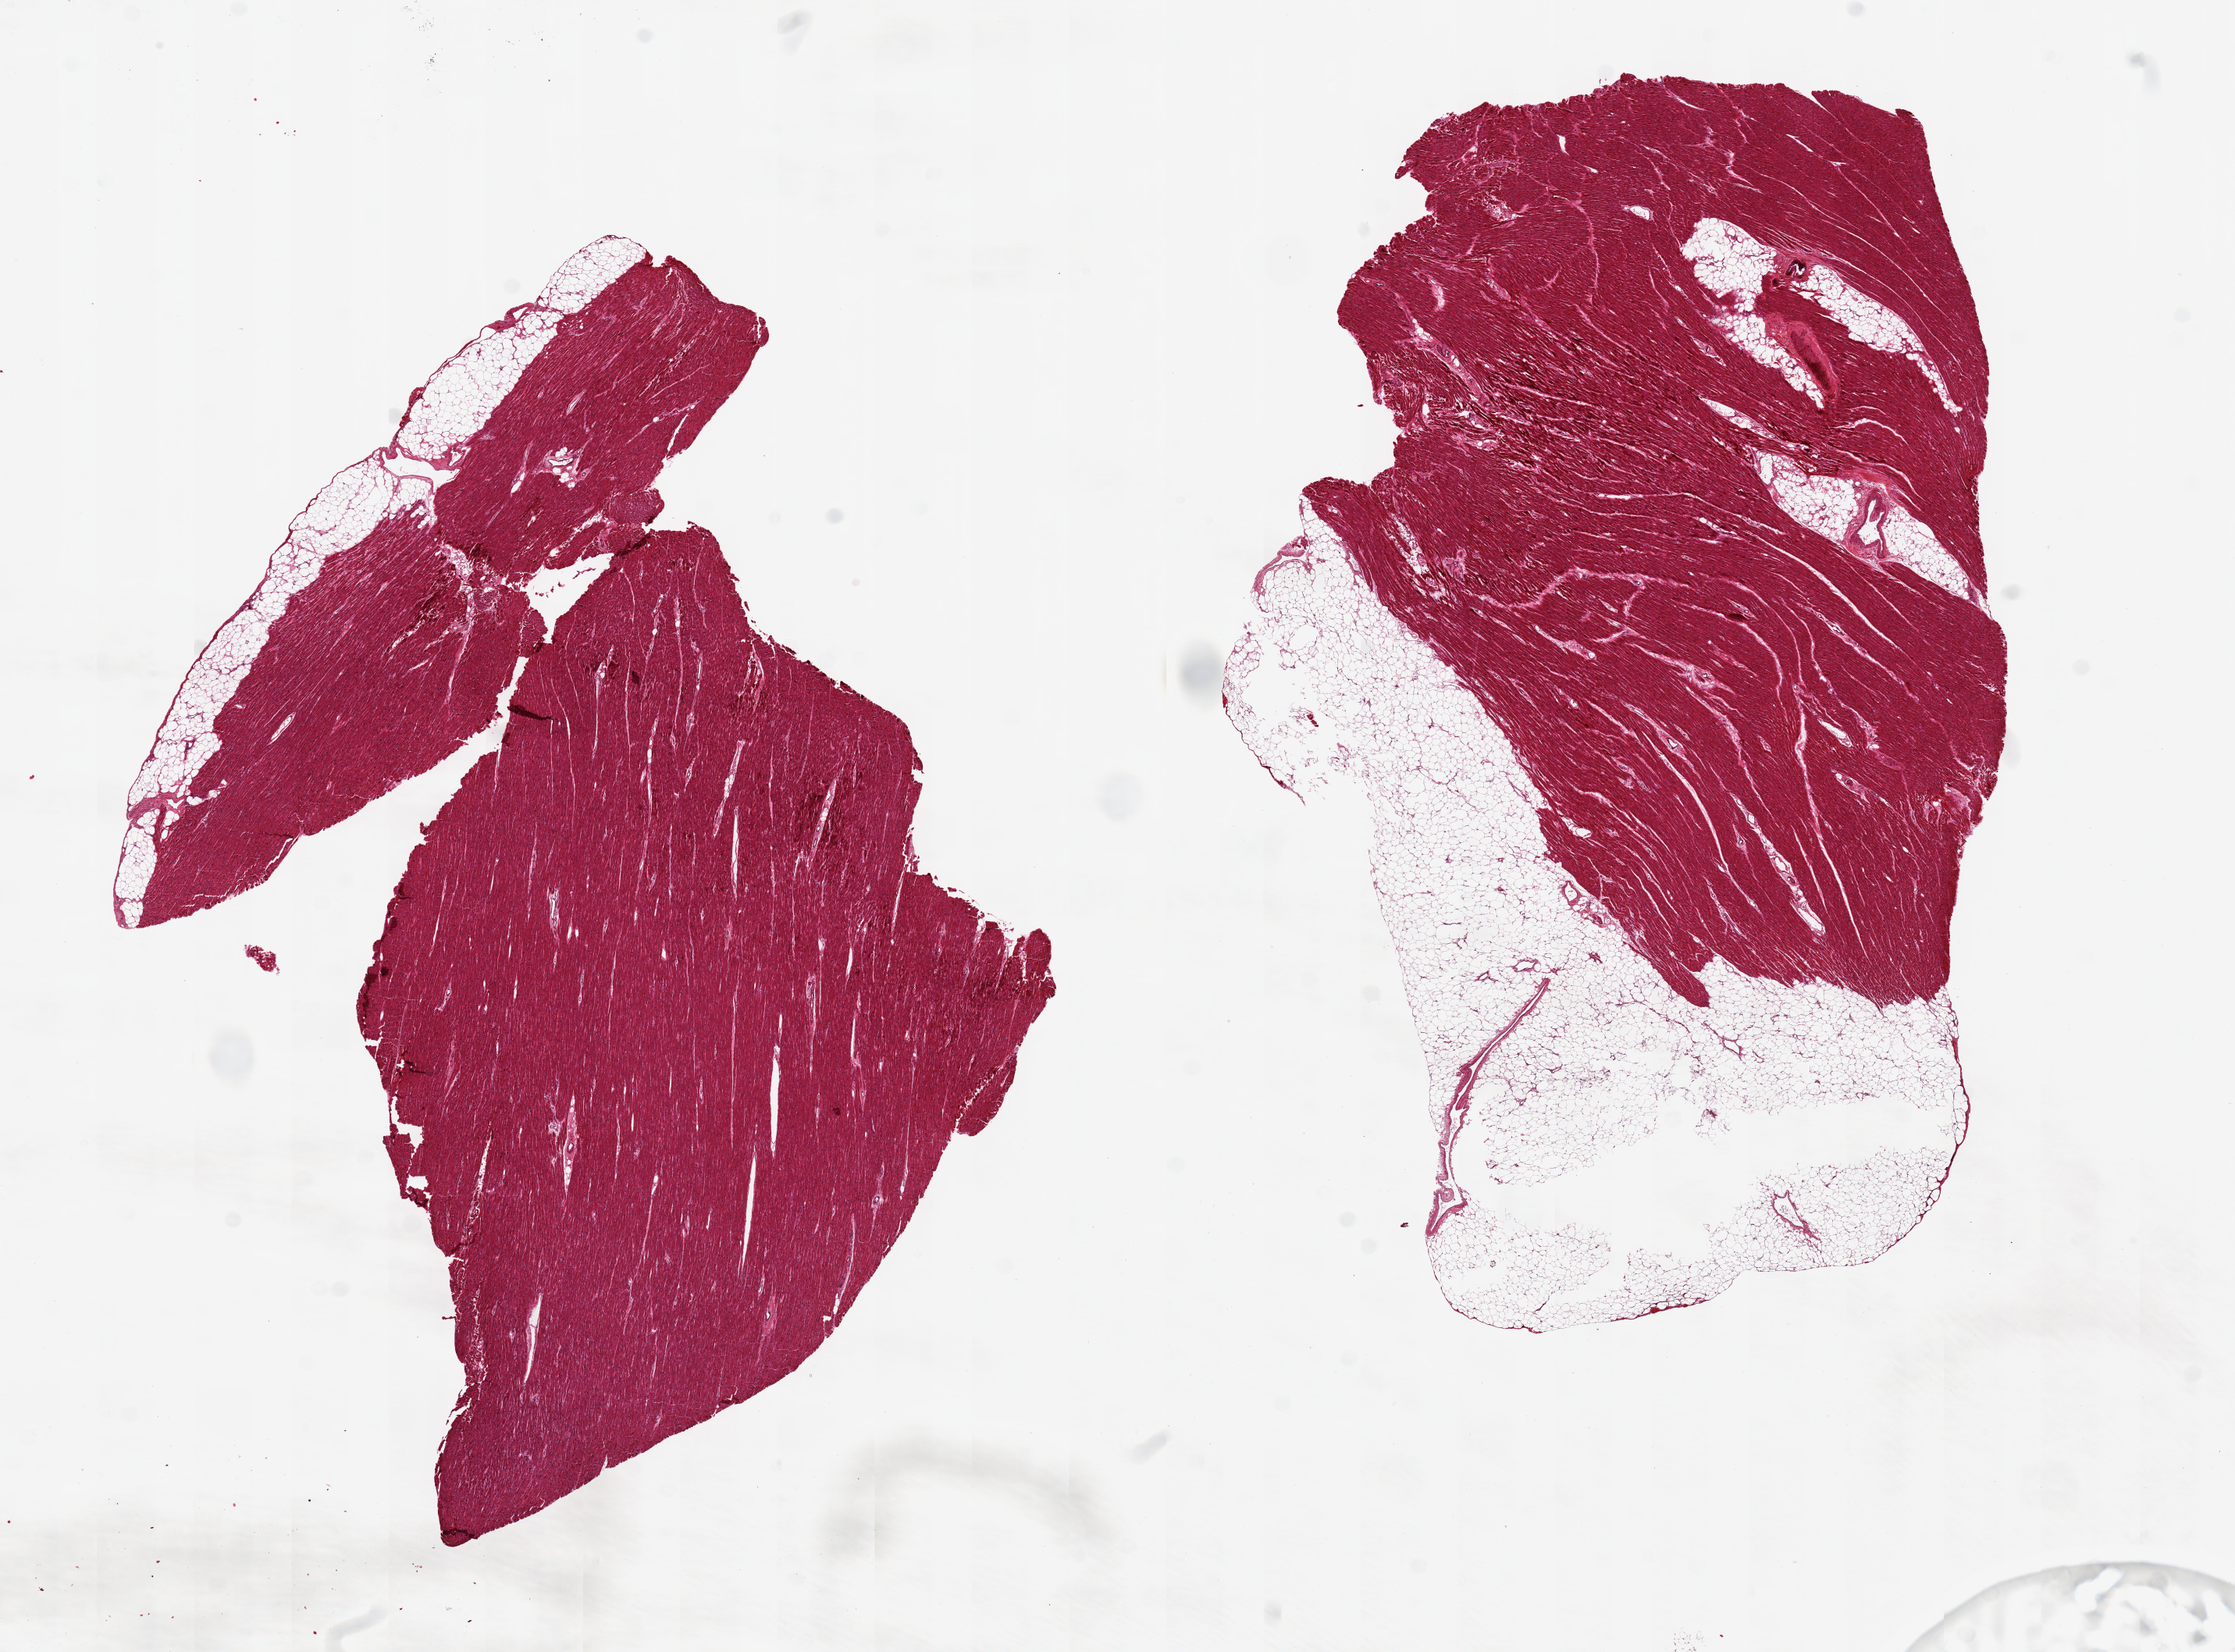
Digitized haematoxylin and eosin-stained section, shown as a low-resolution overview of the whole scanned area (about 22.6 x 16.7 mm); PAXgene-fixed paraffin-embedded (PFPE) section; target tissue: heart; donor tissue sample. Male donor.
Pathologist's review note for this sample: 2 ~12x7mm pieces; one is ~30% epicardial fat.